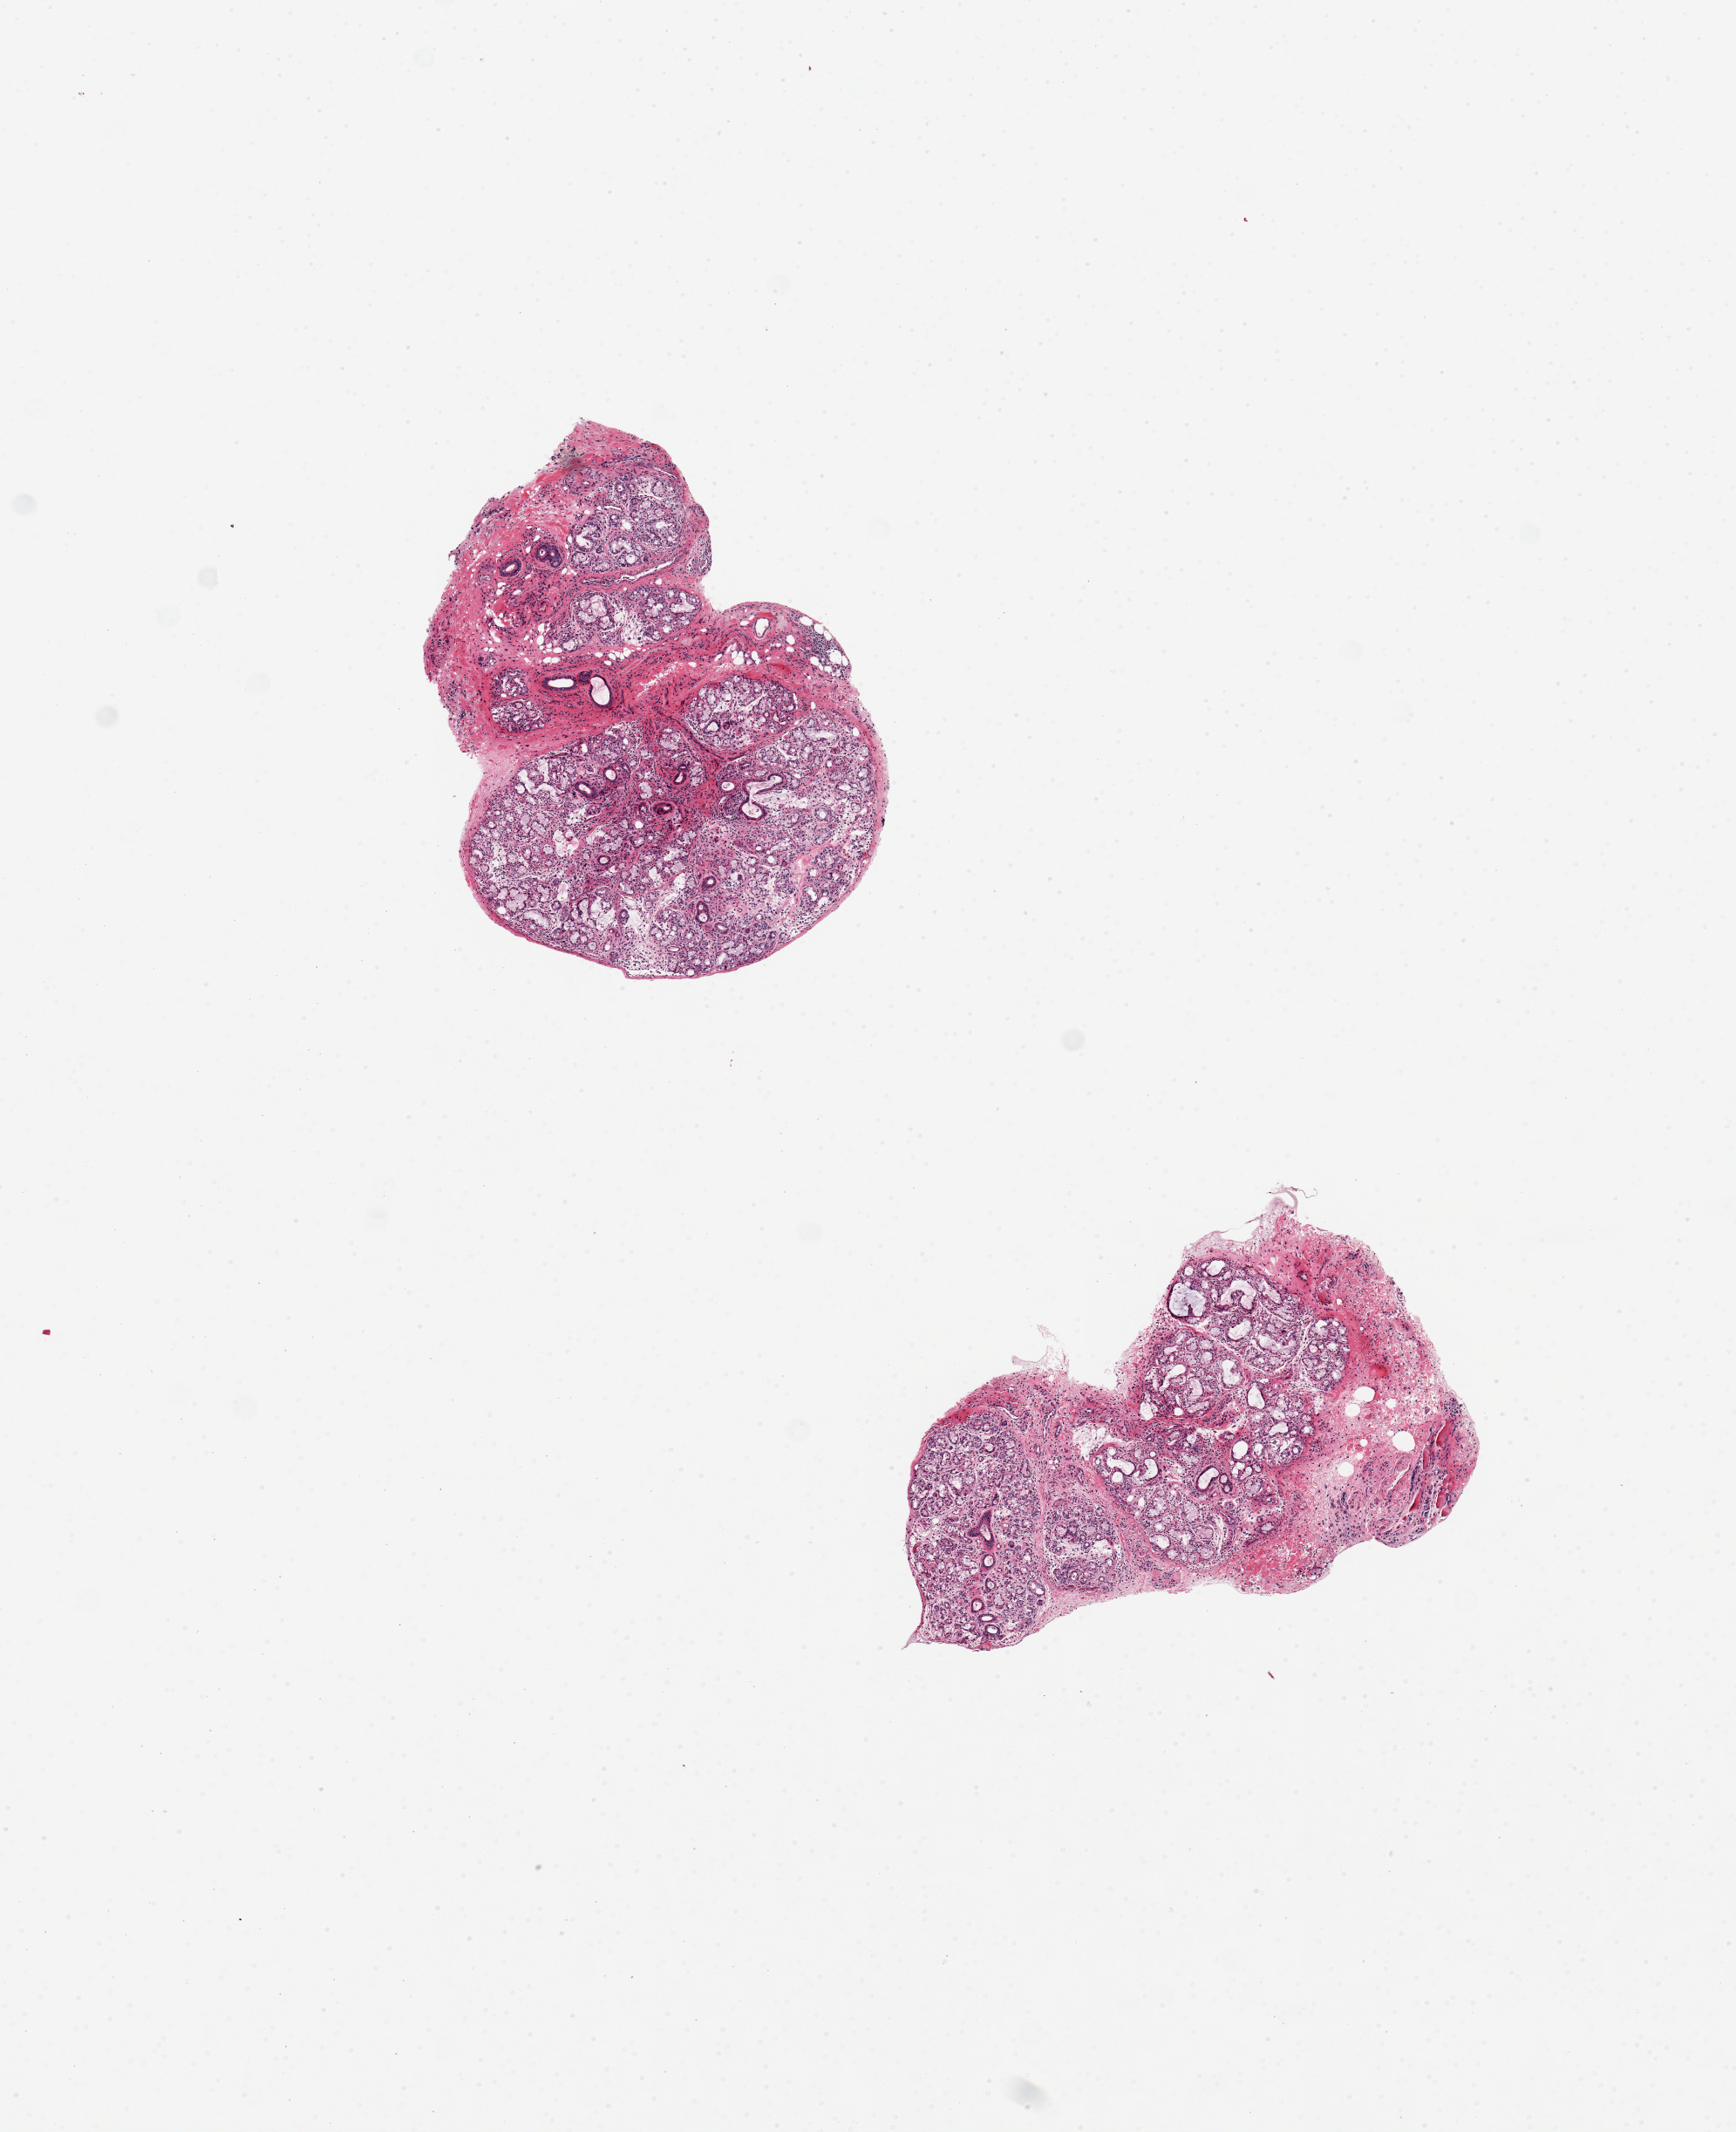
H&E whole-slide image, a low-resolution overview of the entire scanned area, about 7.9 x 9.7 mm. PAXgene-fixed, paraffin-embedded tissue. Target tissue: minor salivary gland. Tissue donor sample. Male donor.
- pathologist's review note for this sample: 2 pieces, well-trimmed